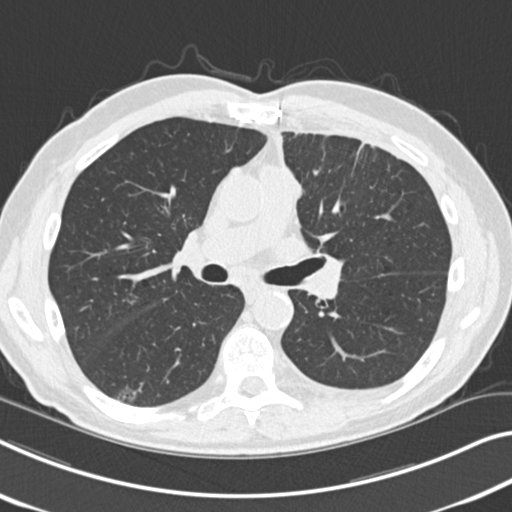
Low-dose screening chest CT, axial slice, first (baseline) screen, lung window (W 1500 / L -600 HU), 120 kVp, slice 98 of 212 in the series, 512 × 512 image matrix. Male, age 68 years at enrolment. Current smoker at enrolment.
• Expert reader's lesion annotation, box from (x=98, y=379) to (x=148, y=413) px.
• Screening reader's record for this exam (one nodule recorded; not confirmed to be the boxed lesion): non-calcified nodule or mass ≥4 mm, right lower lobe, 14 × 10 mm, poorly defined margins, ground glass attenuation.